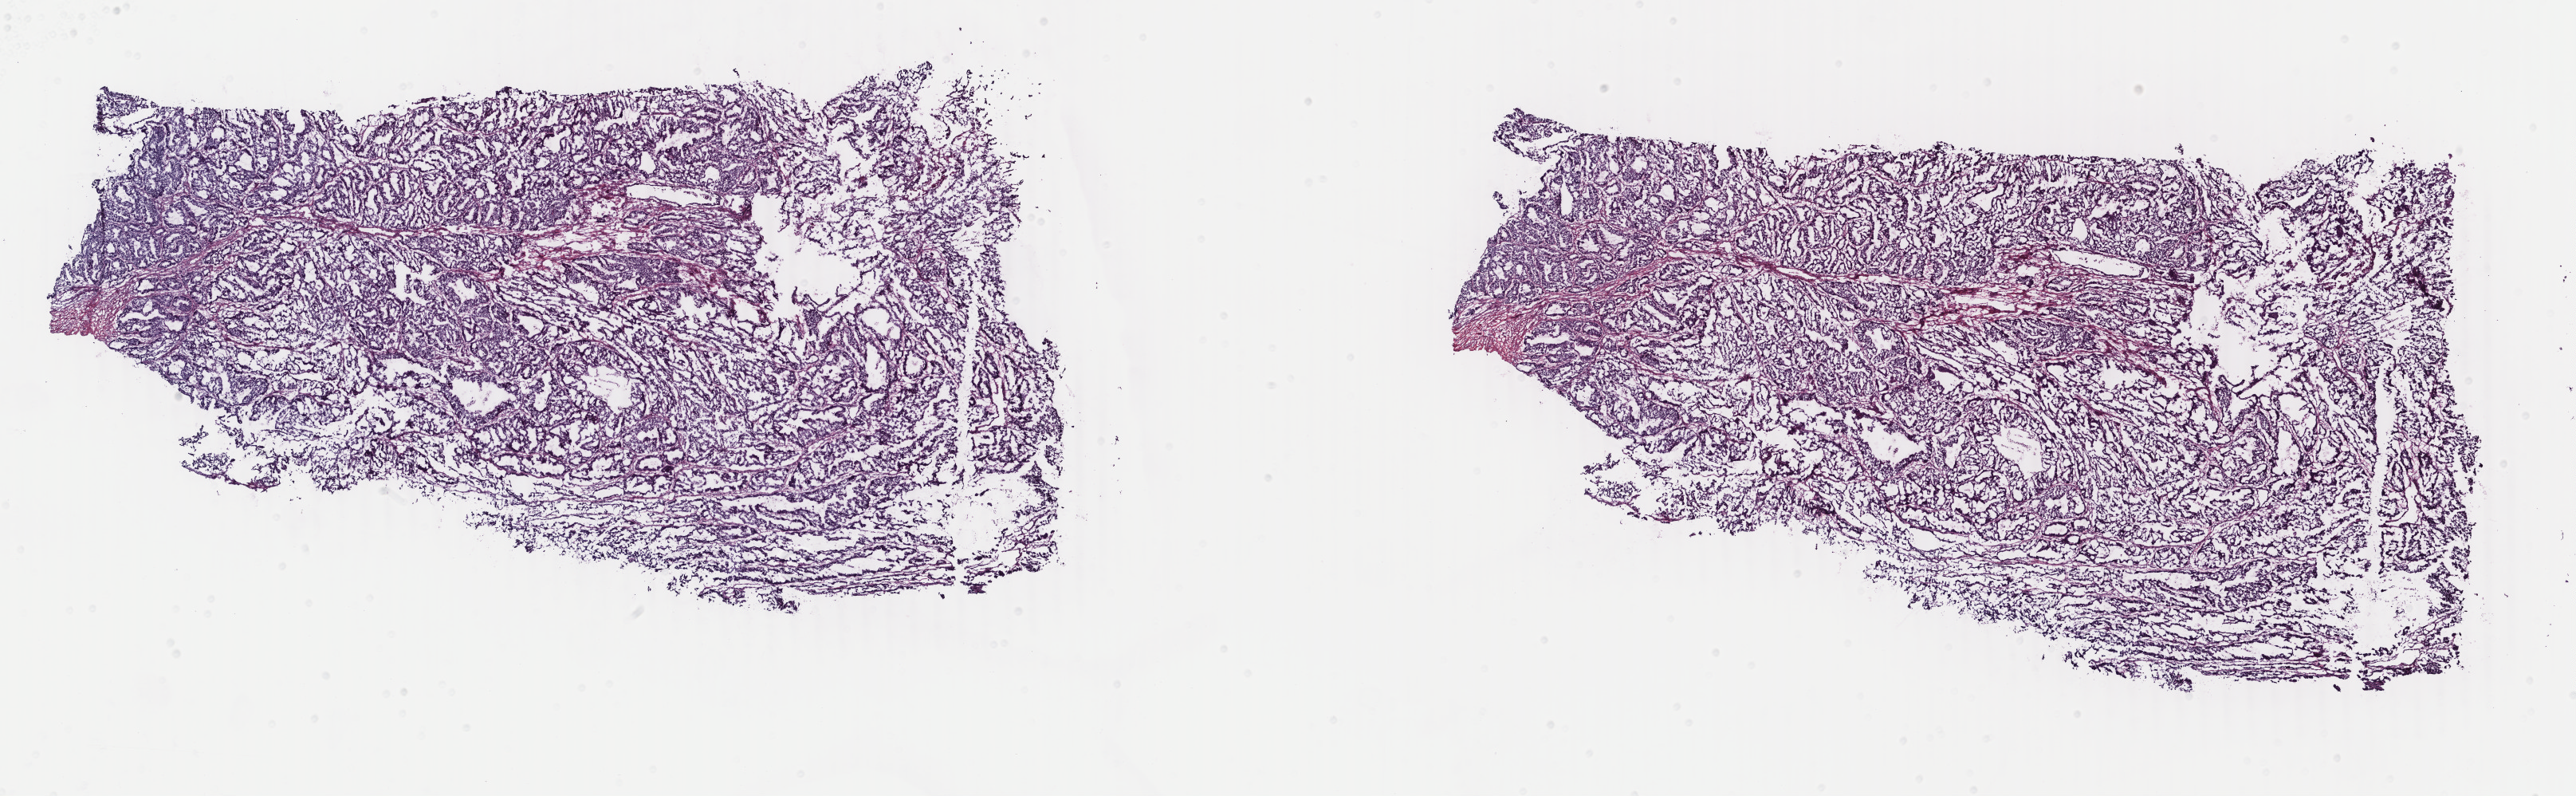
Hematoxylin and eosin (H&E) stained whole-slide image, shown as a low-resolution overview of the whole scanned area (about 25.7 x 7.9 mm, slide scanned at 40x). Frozen section from the top of the tissue portion. Primary tumour sample from the uterus. Female patient; age at initial diagnosis 39 years. Histologic grade: G1 (well differentiated). Slide review estimates, as recorded: tumour cells 100%, tumour nuclei 85%, normal cells 0%, stromal cells 0%, necrosis 0%. Inflammatory infiltration, as recorded: lymphocyte infiltration 0%, monocyte infiltration 0%, neutrophil infiltration 0%.
FIGO stage: IA. Histologic diagnosis: Endometrioid adenocarcinoma, NOS (endometrium).